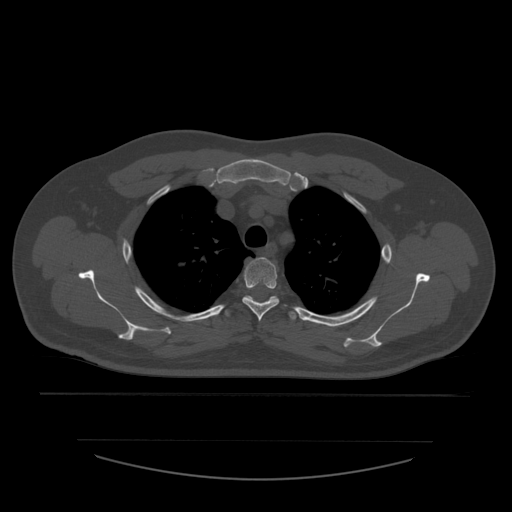
CT including the spine, one axial slice. Position 432 of 532 along the scan axis. 120 kVp. Bone window (W 1800 / L 400 HU). 1.25 mm slice thickness. 512 × 512 image matrix, field of view 441 × 441 mm. Patient age 44 years. Case-level facts recorded for this patient, not image findings: primary cancer: soft tissue sarcoma.
Annotated regions visible in this slice (semi-automatically segmented with operator editing):
- T3 vertebra: bounding box (x1, y1, x2, y2) in pixels: (242, 258, 280, 322)
- T4 vertebra: (225, 296, 297, 320)